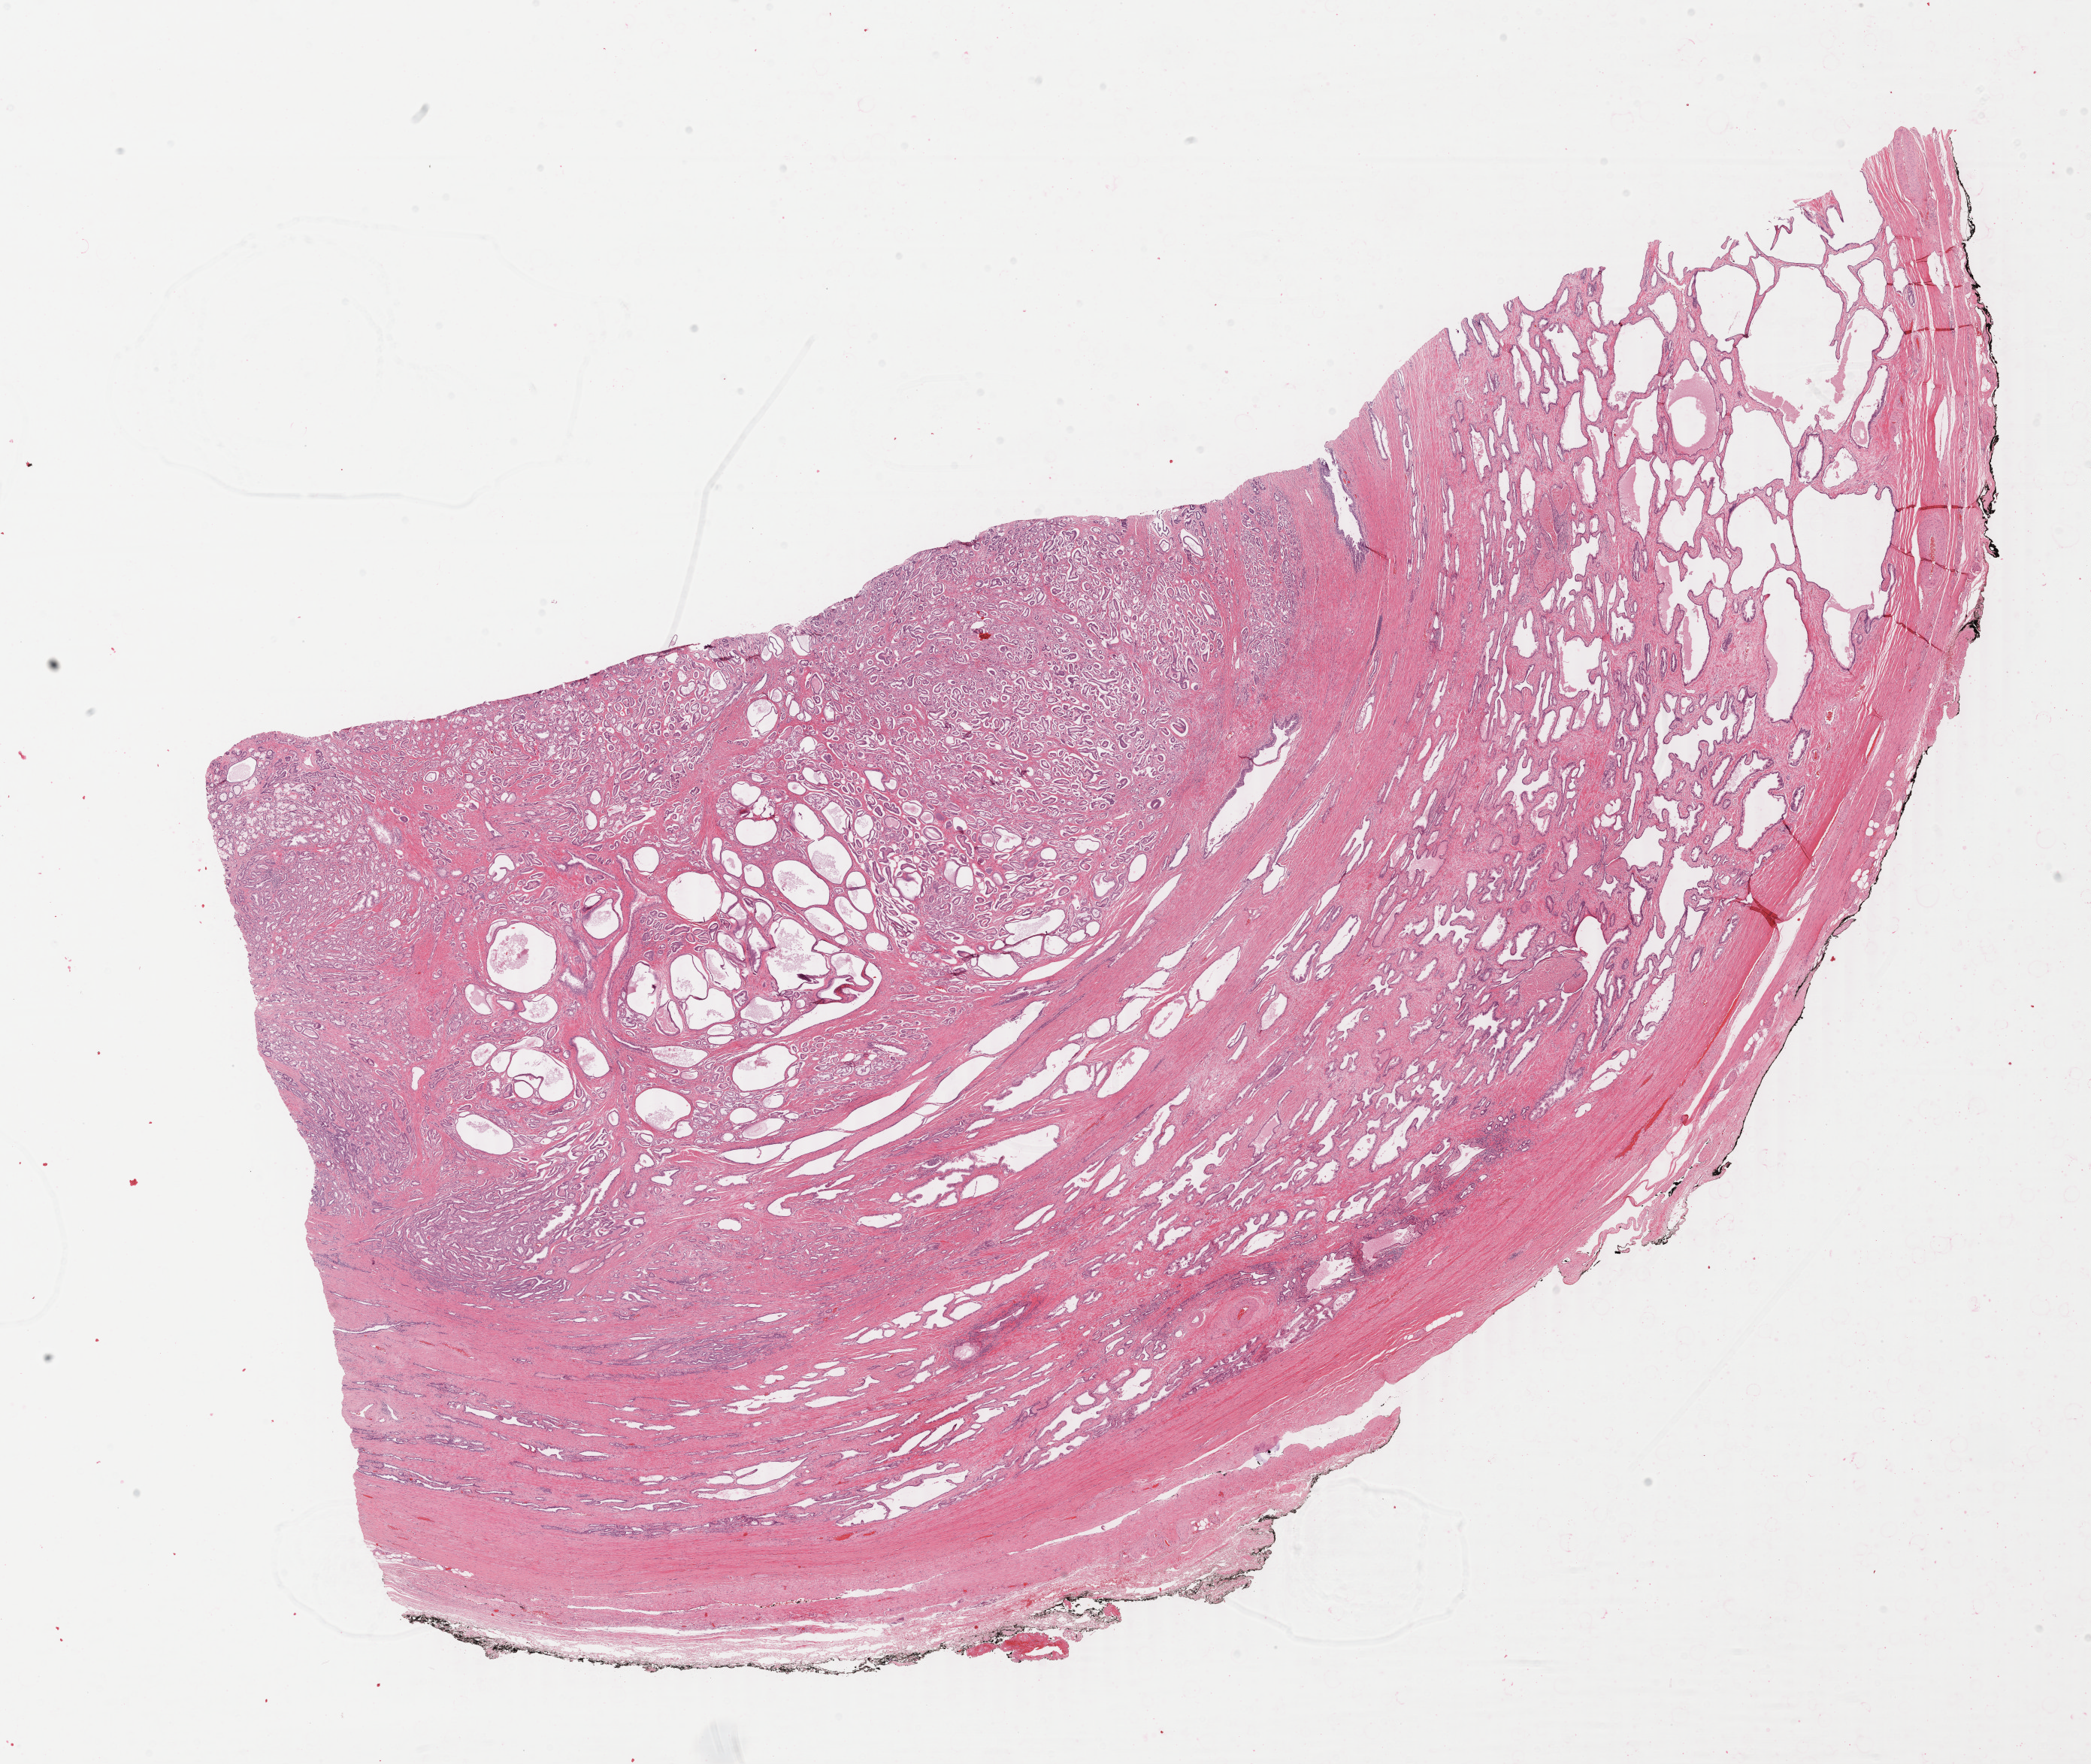
Whole-slide histology image, H&E — shown as a low-resolution overview of the whole scanned area (about 22.1 x 18.7 mm, slide scanned at 40x), FFPE section, sample: primary tumour, prostate. Male patient; age at initial diagnosis 53 years. Gleason score: 7 (3+4).
Laterality: bilateral. Pathologic diagnosis: Adenocarcinoma, NOS (prostate gland).